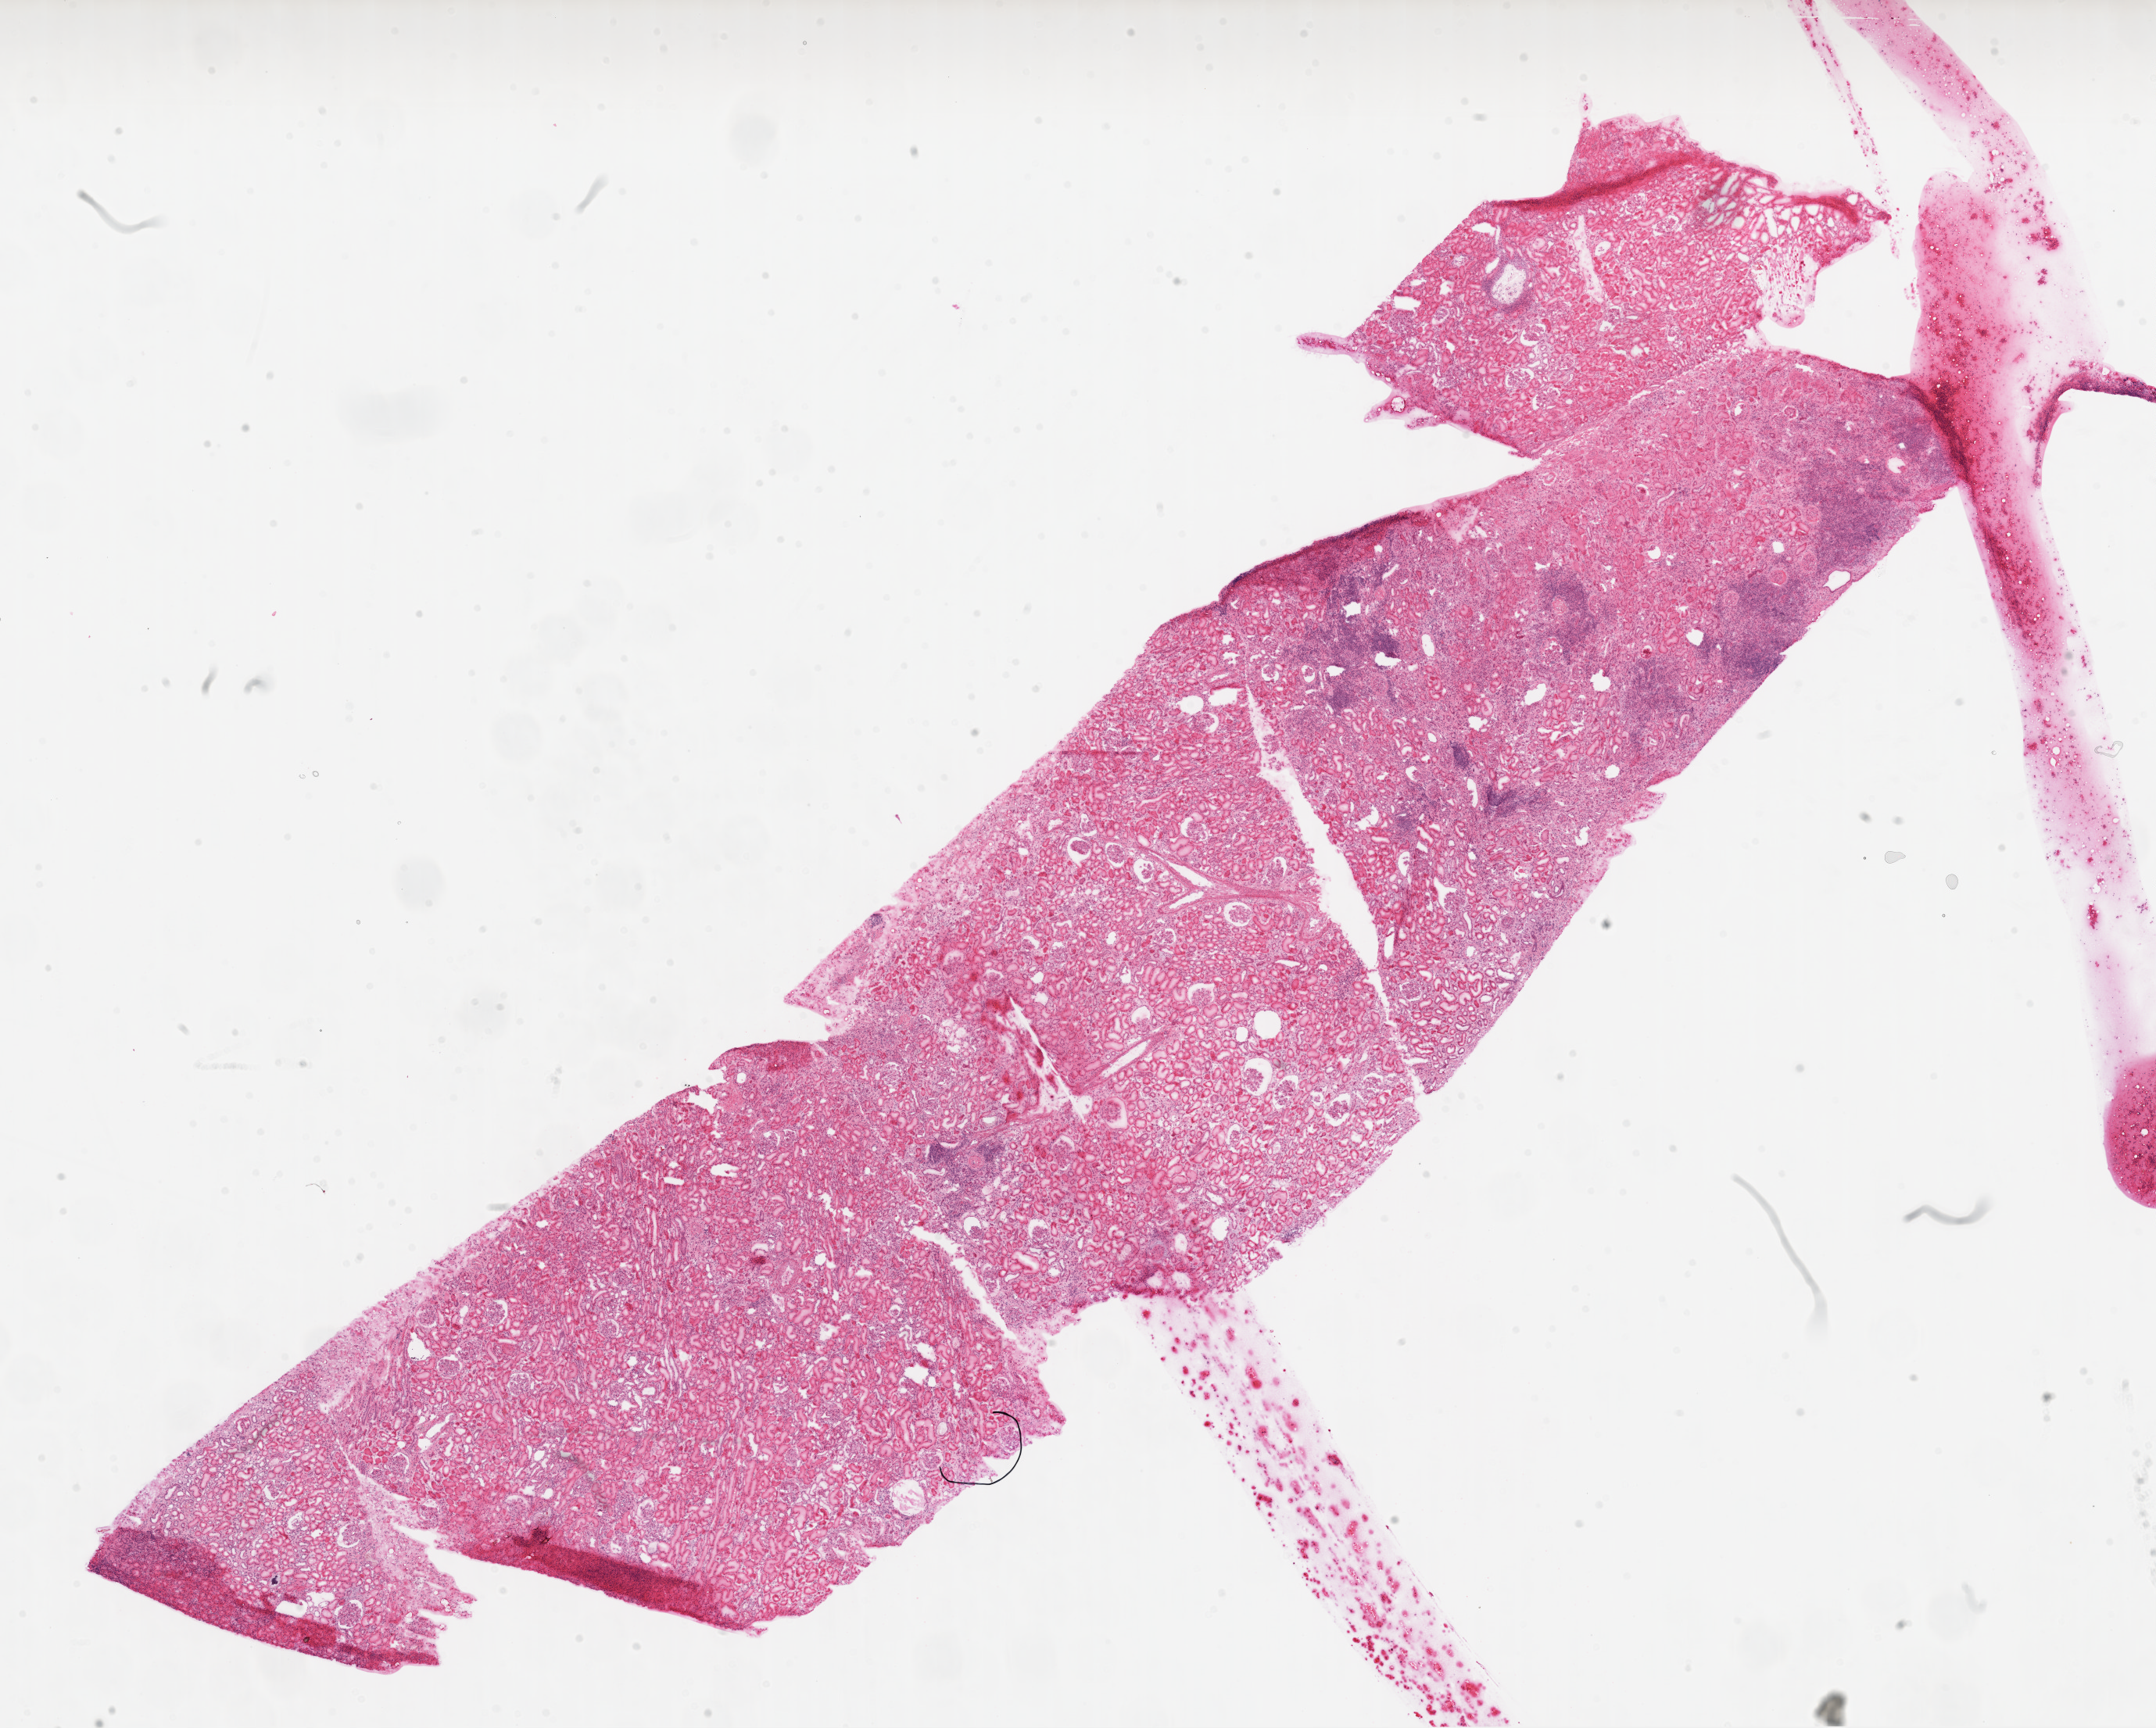
Whole-slide histology image, H&E-stained — shown as a low-resolution overview of the whole scanned area (about 22.2 x 17.8 mm), frozen section from the top of the tissue portion, kidney, solid tissue normal (non-tumour tissue) sample. Patient: male, age at initial diagnosis 47 years.
- this section: solid tissue normal (non-tumour) sample from the same patient
- patient diagnosis: Clear cell adenocarcinoma, NOS